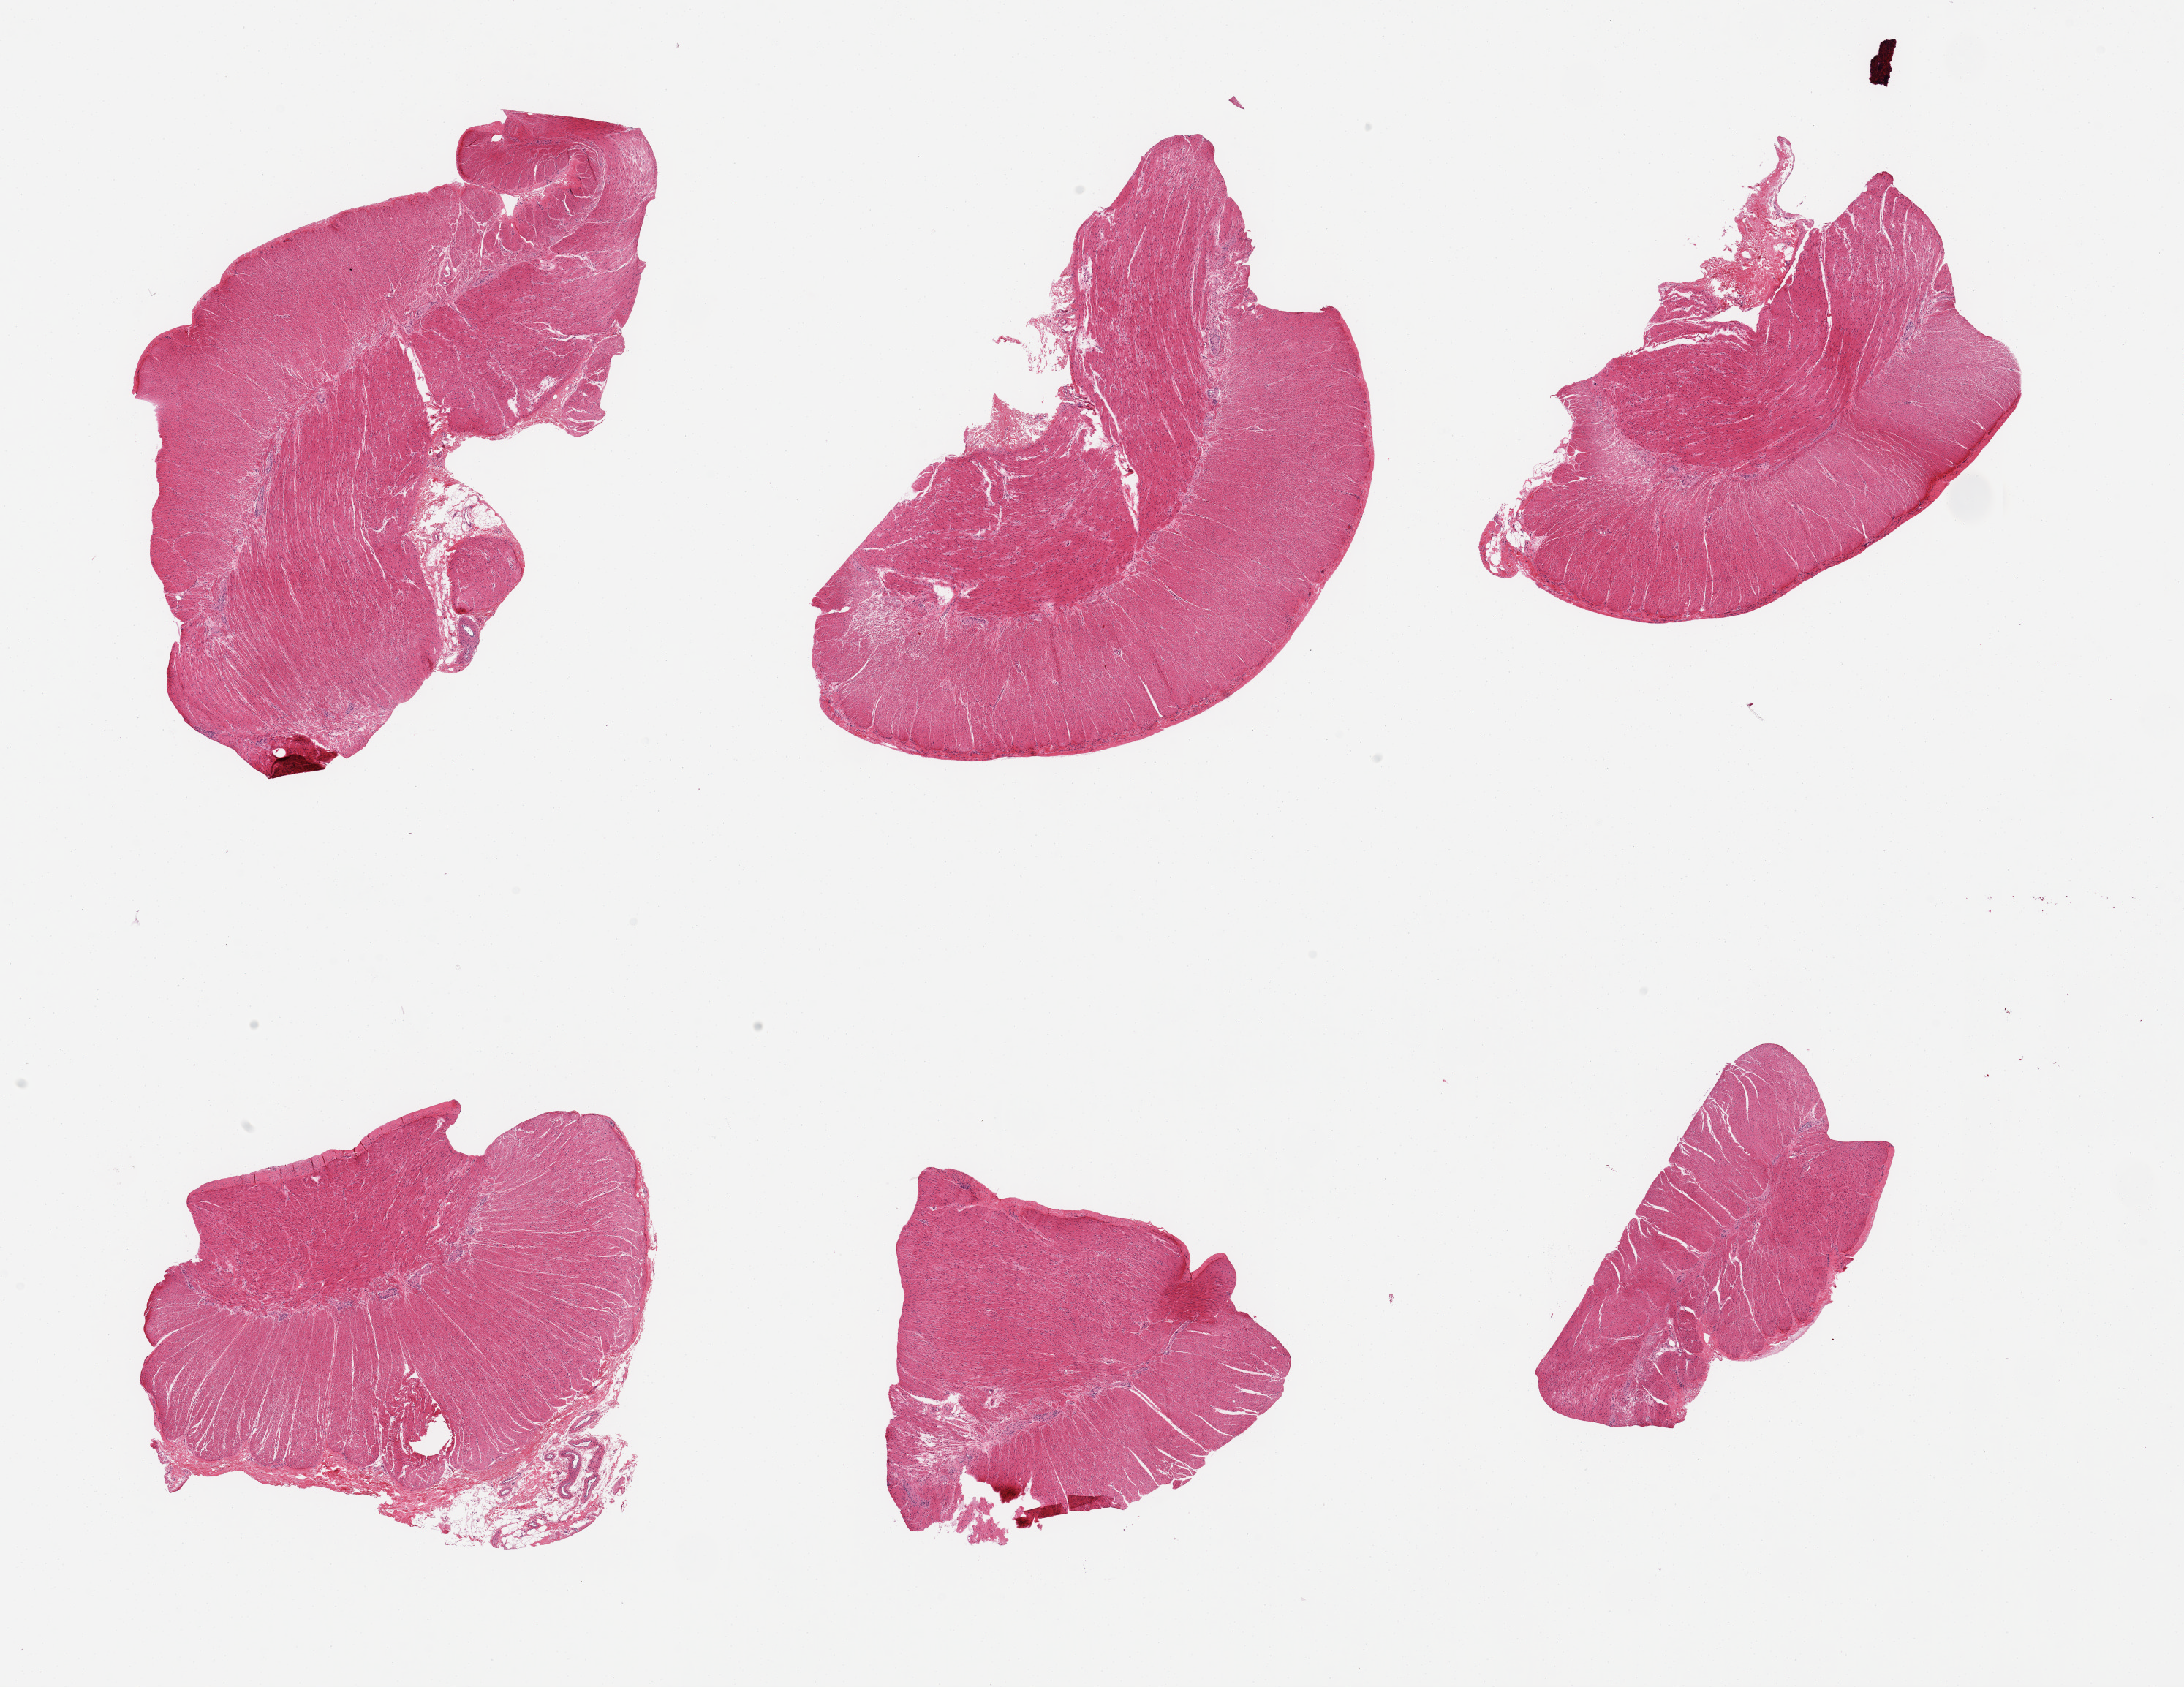
Hematoxylin and eosin (H&E) whole-slide image, low-resolution overview of the scanned area, about 23.6 x 18.2 mm (from a 20x scan); PAXgene-fixed paraffin-embedded (PFPE) section; sampled site (target tissue): sigmoid colon; tissue donor sample. Male donor.
Reviewer comment on this tissue sample: 6 pieces; target muscularis.